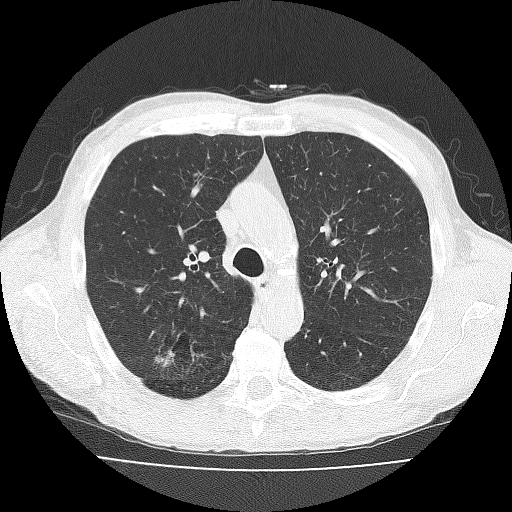
Axial slice from a low-dose chest CT screening exam; third annual screen; lung window (W 1500 / L -600 HU); 2 mm slice thickness; 120 kVp; slice 58 of 181 in the series. Male participant, aged 73 years at enrolment.
Lesion marked by an expert reader, bounding box <140,334,190,379> (left, top, right, bottom; pixels). Screening reader's record for this exam (one nodule recorded; not confirmed to be the boxed lesion): non-calcified nodule or mass ≥4 mm, right upper lobe, 11 × 10 mm, spiculated (stellate) margins, soft tissue attenuation, pre-existing on the prior screen: no. Official screen result: positive, other. Participant outcome: lung cancer diagnosed 38 days after this screen — adenosquamous carcinoma, right upper lobe, well differentiated (G1), stage IA (AJCC 6th edition), 20 mm at pathology.